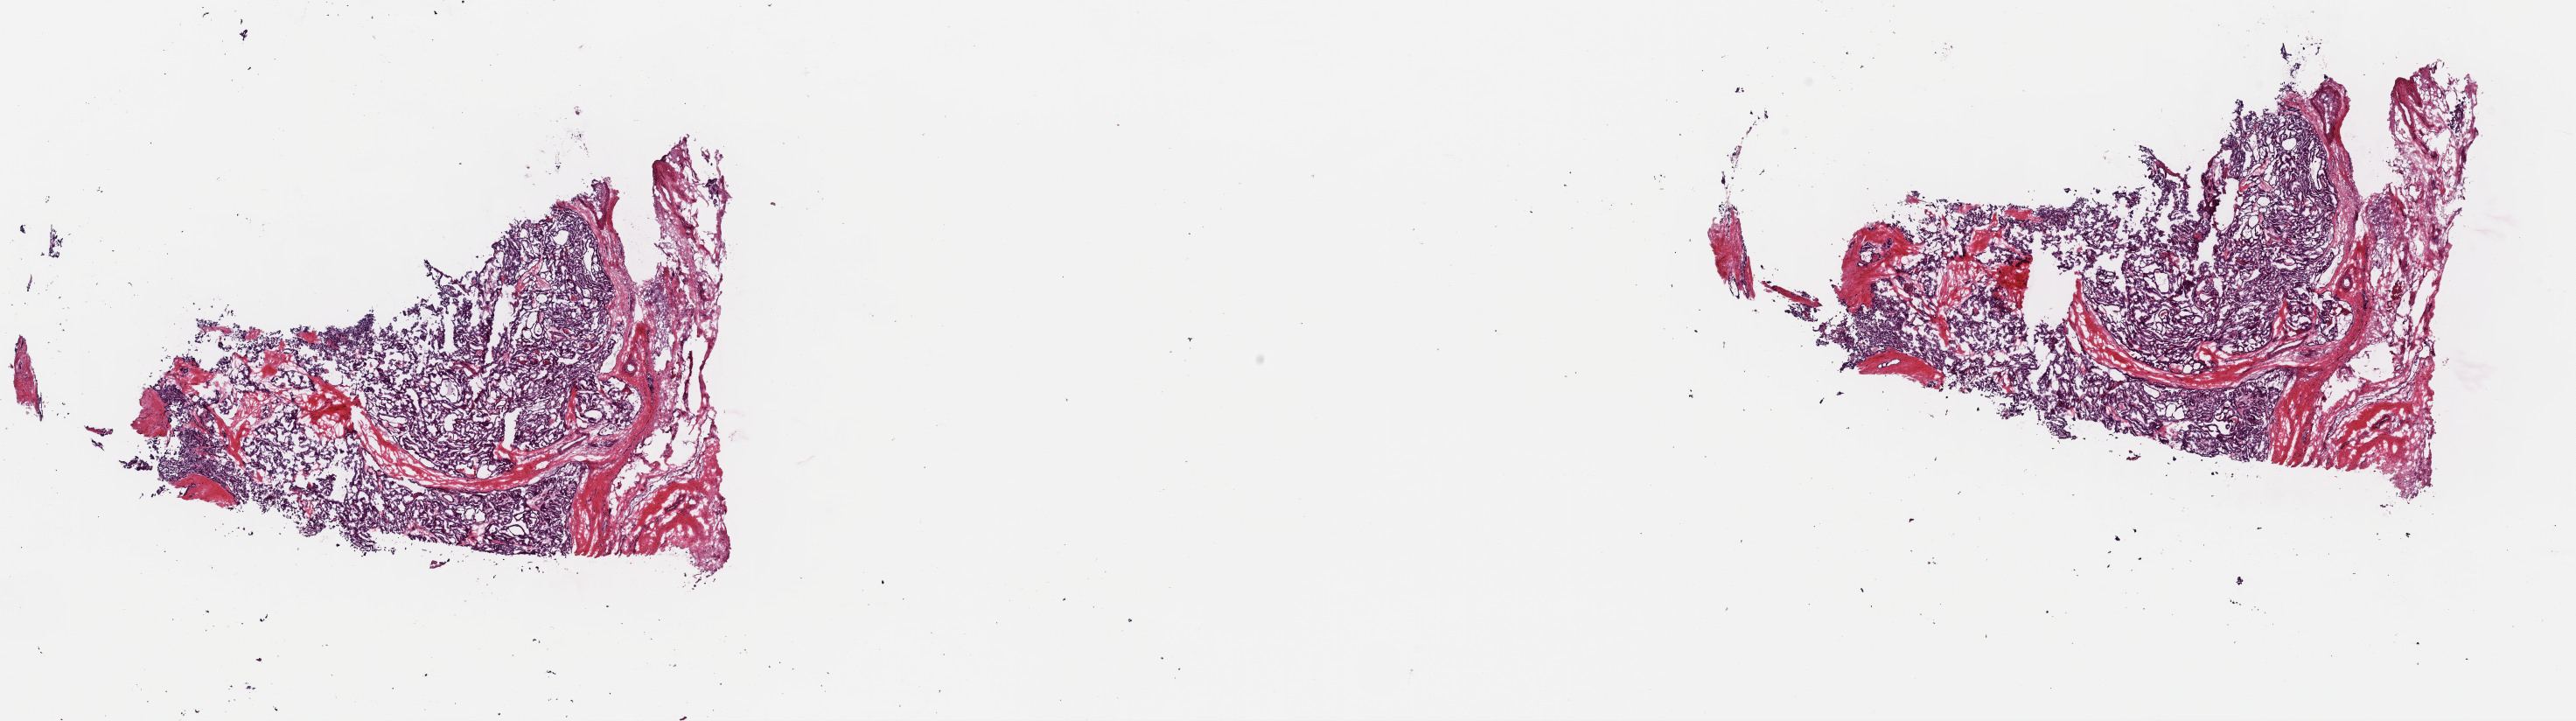
Digitized H&E tissue section (whole slide) — a low-resolution overview of the entire scanned area, about 23.3 x 6.5 mm, frozen section from the top of the tissue portion, primary tumour sample from the thyroid. Female, age 62 years at initial diagnosis. Pathologist review of this section (percent, as recorded): tumour cells 90%, tumour nuclei 92%, normal cells 0%, stromal cells 10%, necrosis 0%. Inflammatory infiltration, as recorded: lymphocyte infiltration 0%, monocyte infiltration 0%, neutrophil infiltration 0%.
* pathologic diagnosis: Papillary adenocarcinoma, NOS (thyroid gland)
* lymph nodes positive (case pathology): 0 of 20 examined
* AJCC pathologic stage: IVA (6th edition)